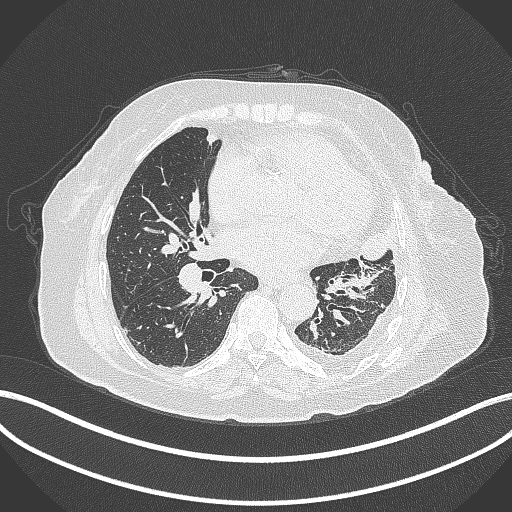
Chest CT, one axial slice; slice 168 of 399 in the series (ordered by position); reconstruction kernel B70f; 120 kVp; lung window (W 1500 / L -600 HU); 1 mm slice thickness; 512 × 512 image matrix. Female patient, age 75 years. From the clinical record (not read from this slice): clinical TNM (as recorded): T3 N3 M1.
Annotated regions visible in this slice (rectangle marked by the reading radiologist):
- lung tumour (recorded histology: adenocarcinoma): bounding box <355,219,399,265> (left, top, right, bottom; pixels)